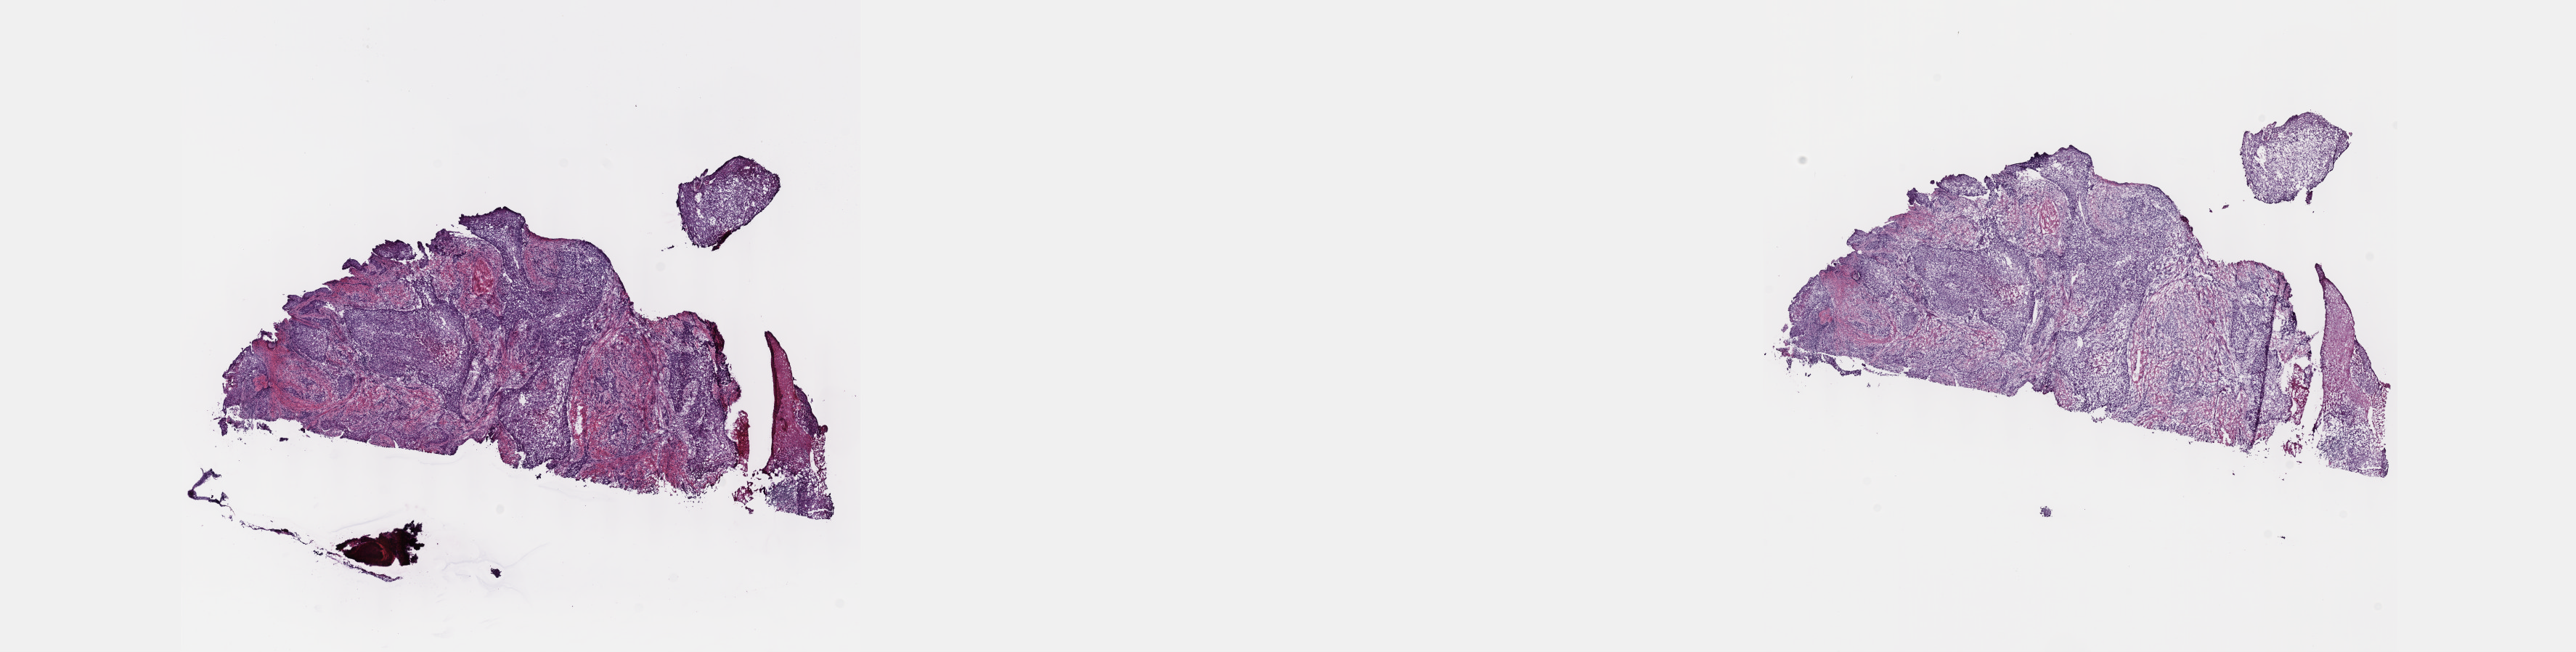
Digitized H&E tissue section (whole slide) — whole scanned area (about 28.7 x 7.3 mm, acquisition: 40x scan) shown as a low-resolution overview, frozen section from the top of the tissue portion, sample: primary tumour, head and neck. Male patient; age at initial diagnosis 52 years. Histologic grade: G2 (moderately differentiated). Slide review estimates, as recorded: tumour cells 100%, tumour nuclei 60%, normal cells 0%, stromal cells 0%, necrosis 0%. Infiltration values recorded for this section: lymphocyte infiltration 10%, monocyte infiltration 0%, neutrophil infiltration 0%.
Histologic diagnosis: Squamous cell carcinoma, NOS (larynx, NOS). TNM: T4a N2c MX. AJCC pathologic stage: IVA (7th edition).